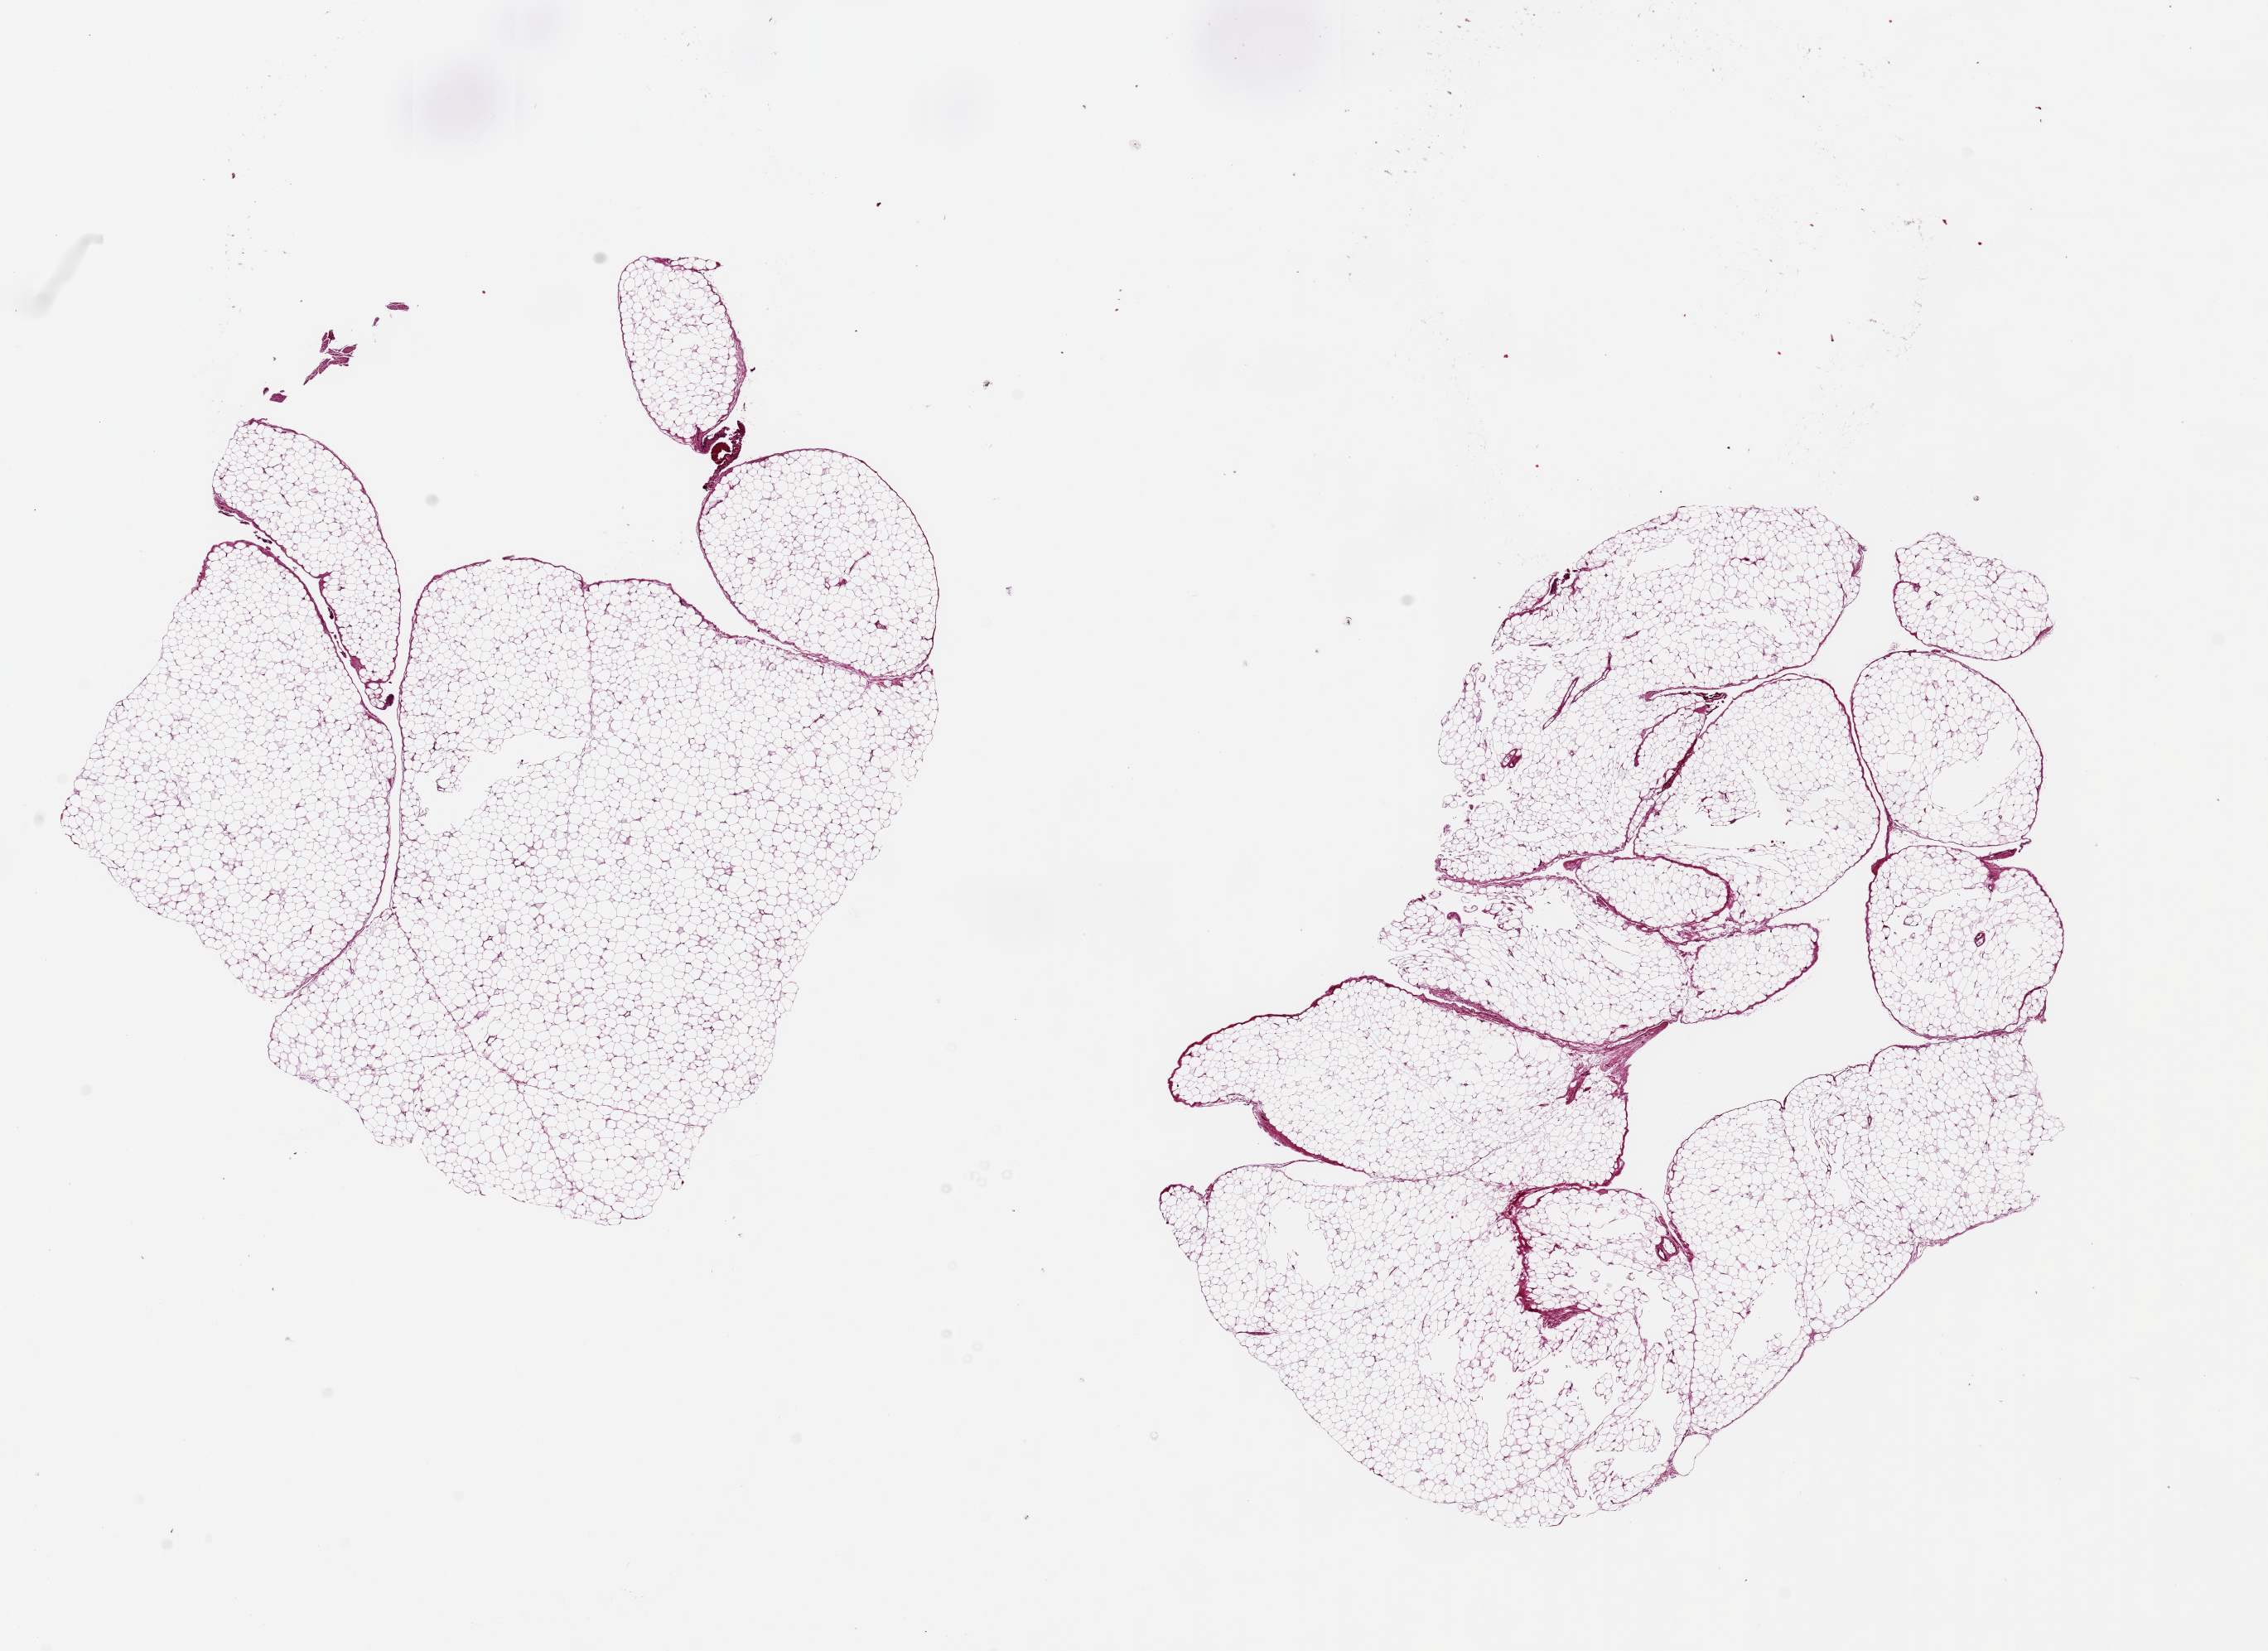
Hematoxylin and eosin (H&E) whole-slide image, shown as a low-resolution overview of the whole scanned area (about 21.7 x 15.8 mm, from a 20x scan), PAXgene-fixed paraffin-embedded (PFPE) section, sampled site (target tissue): omentum, donor tissue sample.
Reviewer comment on this tissue sample: 2 pieces, 9x7 & 10x9mm.